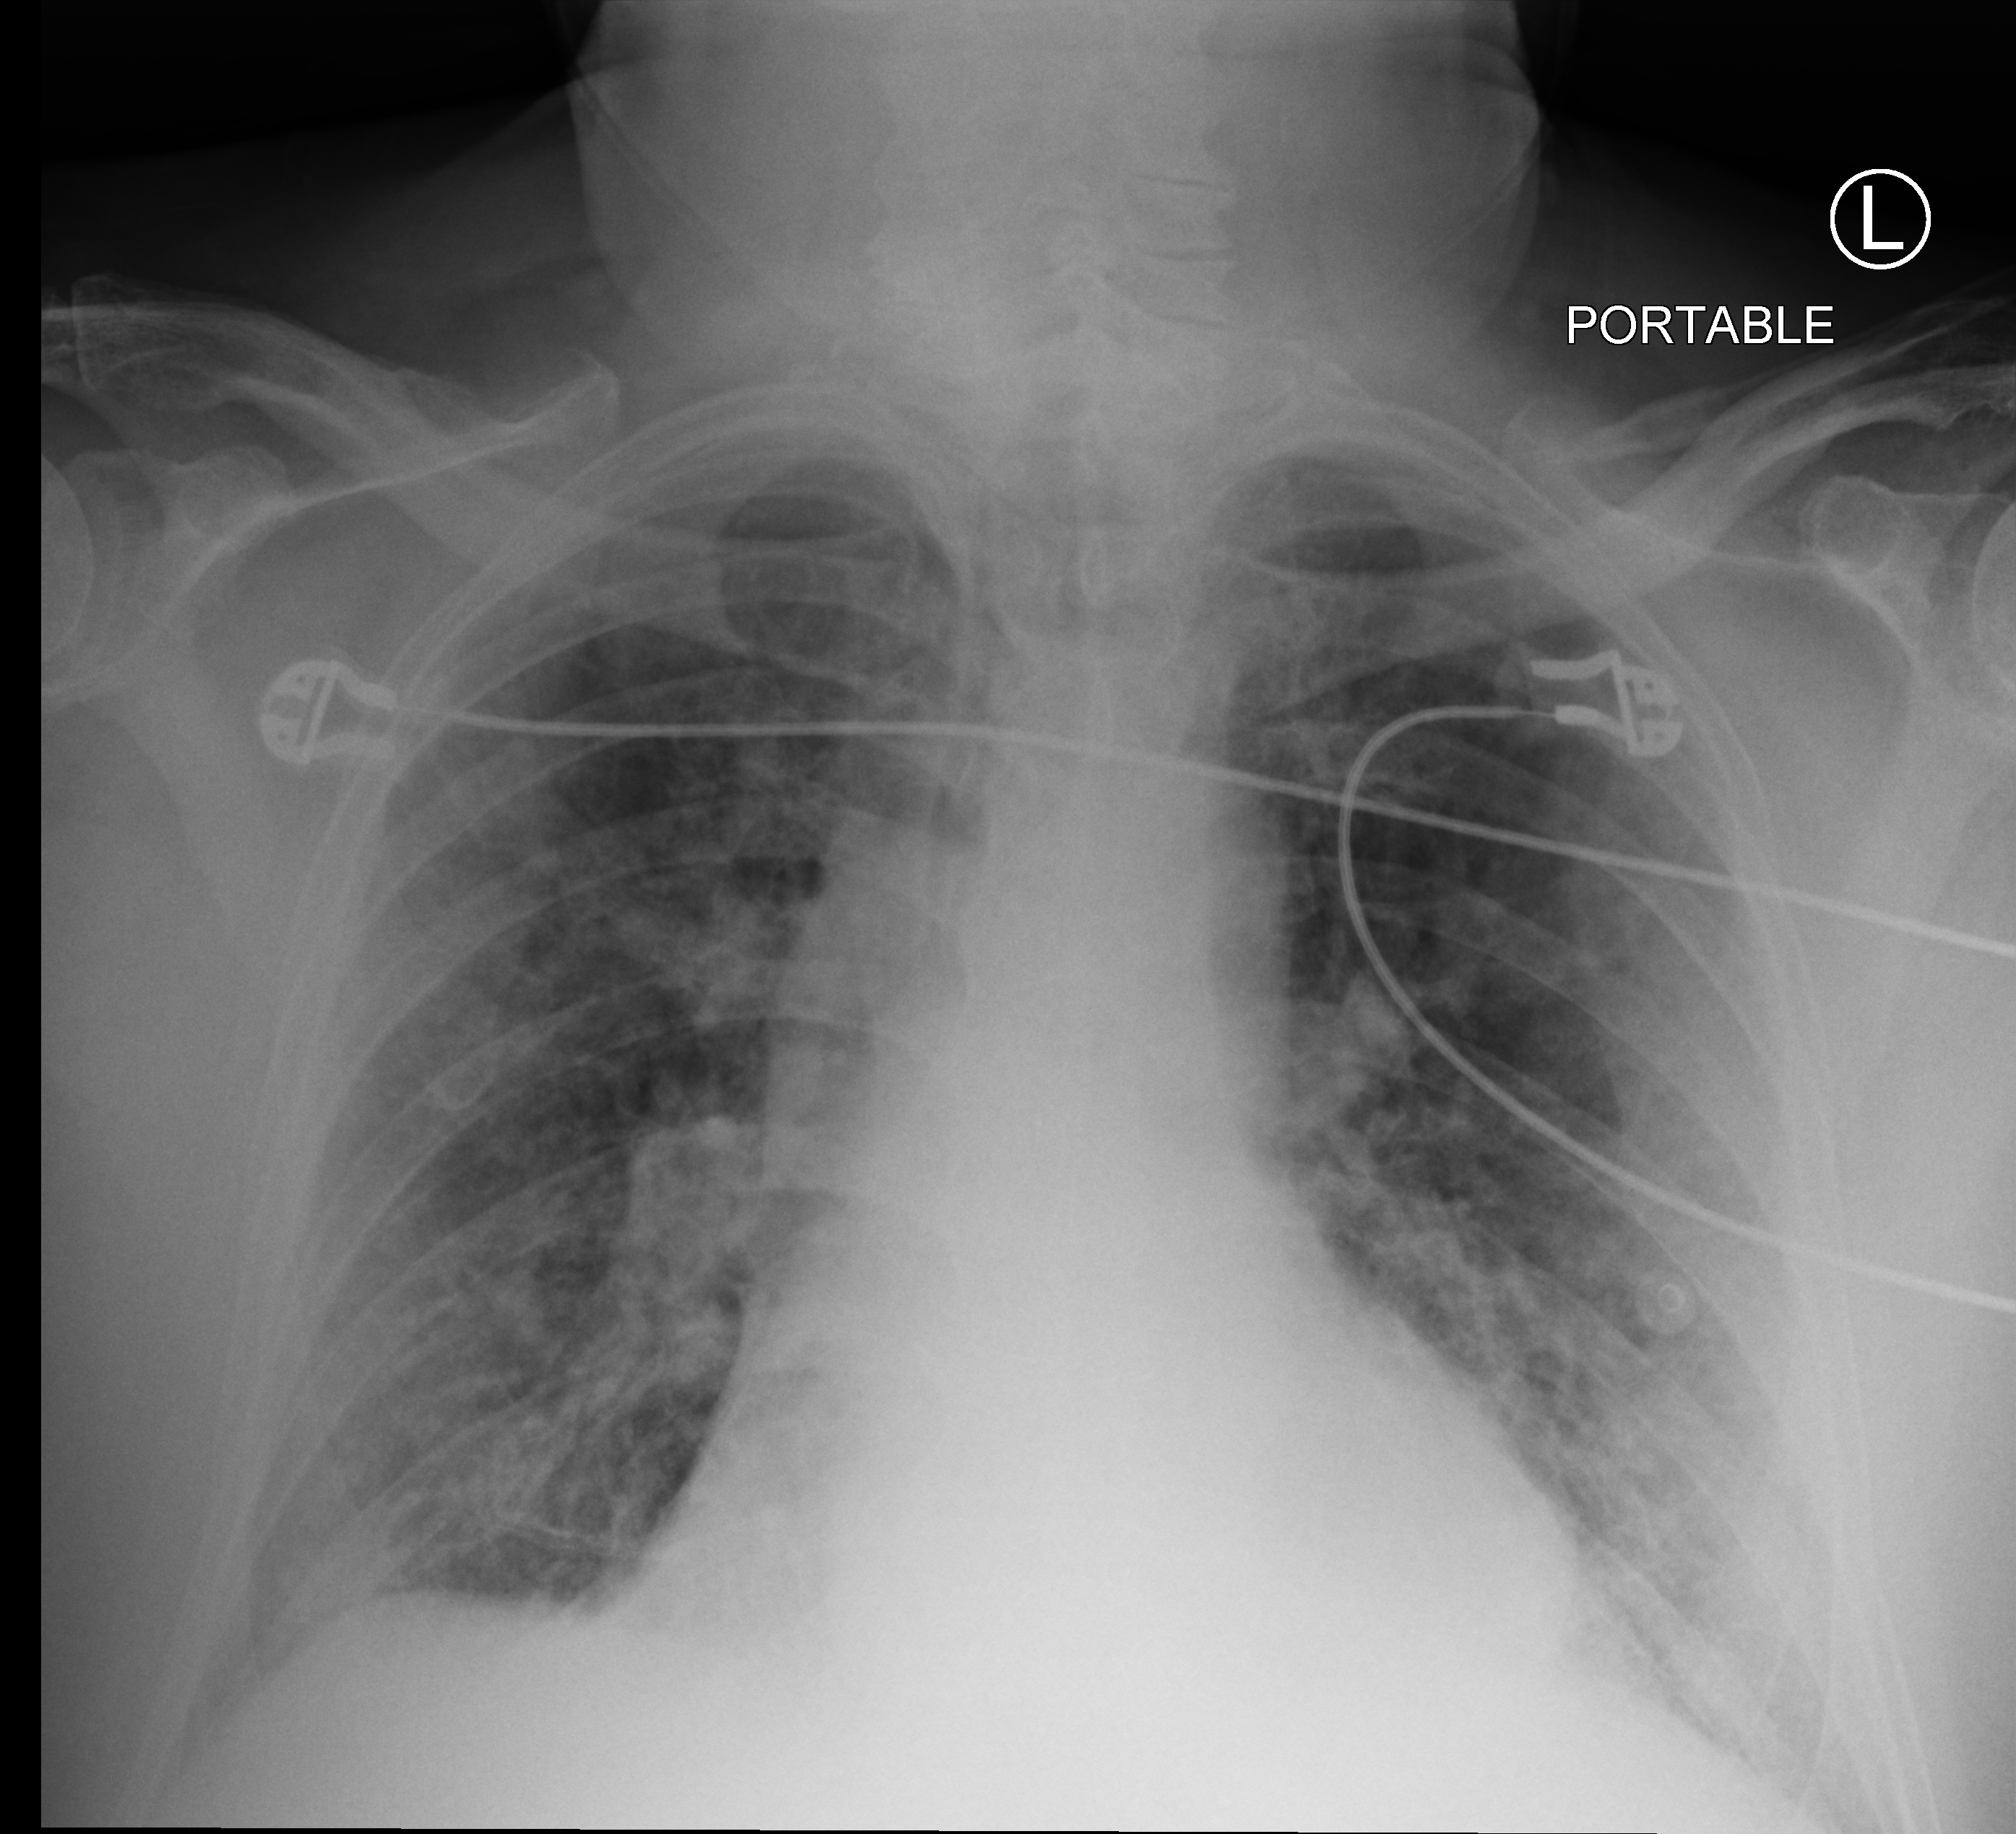
Chest X-ray (portable). Male patient hospitalised with COVID-19, age 75–90 years.
From the hospital-stay record, not from the radiograph (when in the stay this image was taken is not recorded):
- admitted to intensive care during this hospital stay: yes